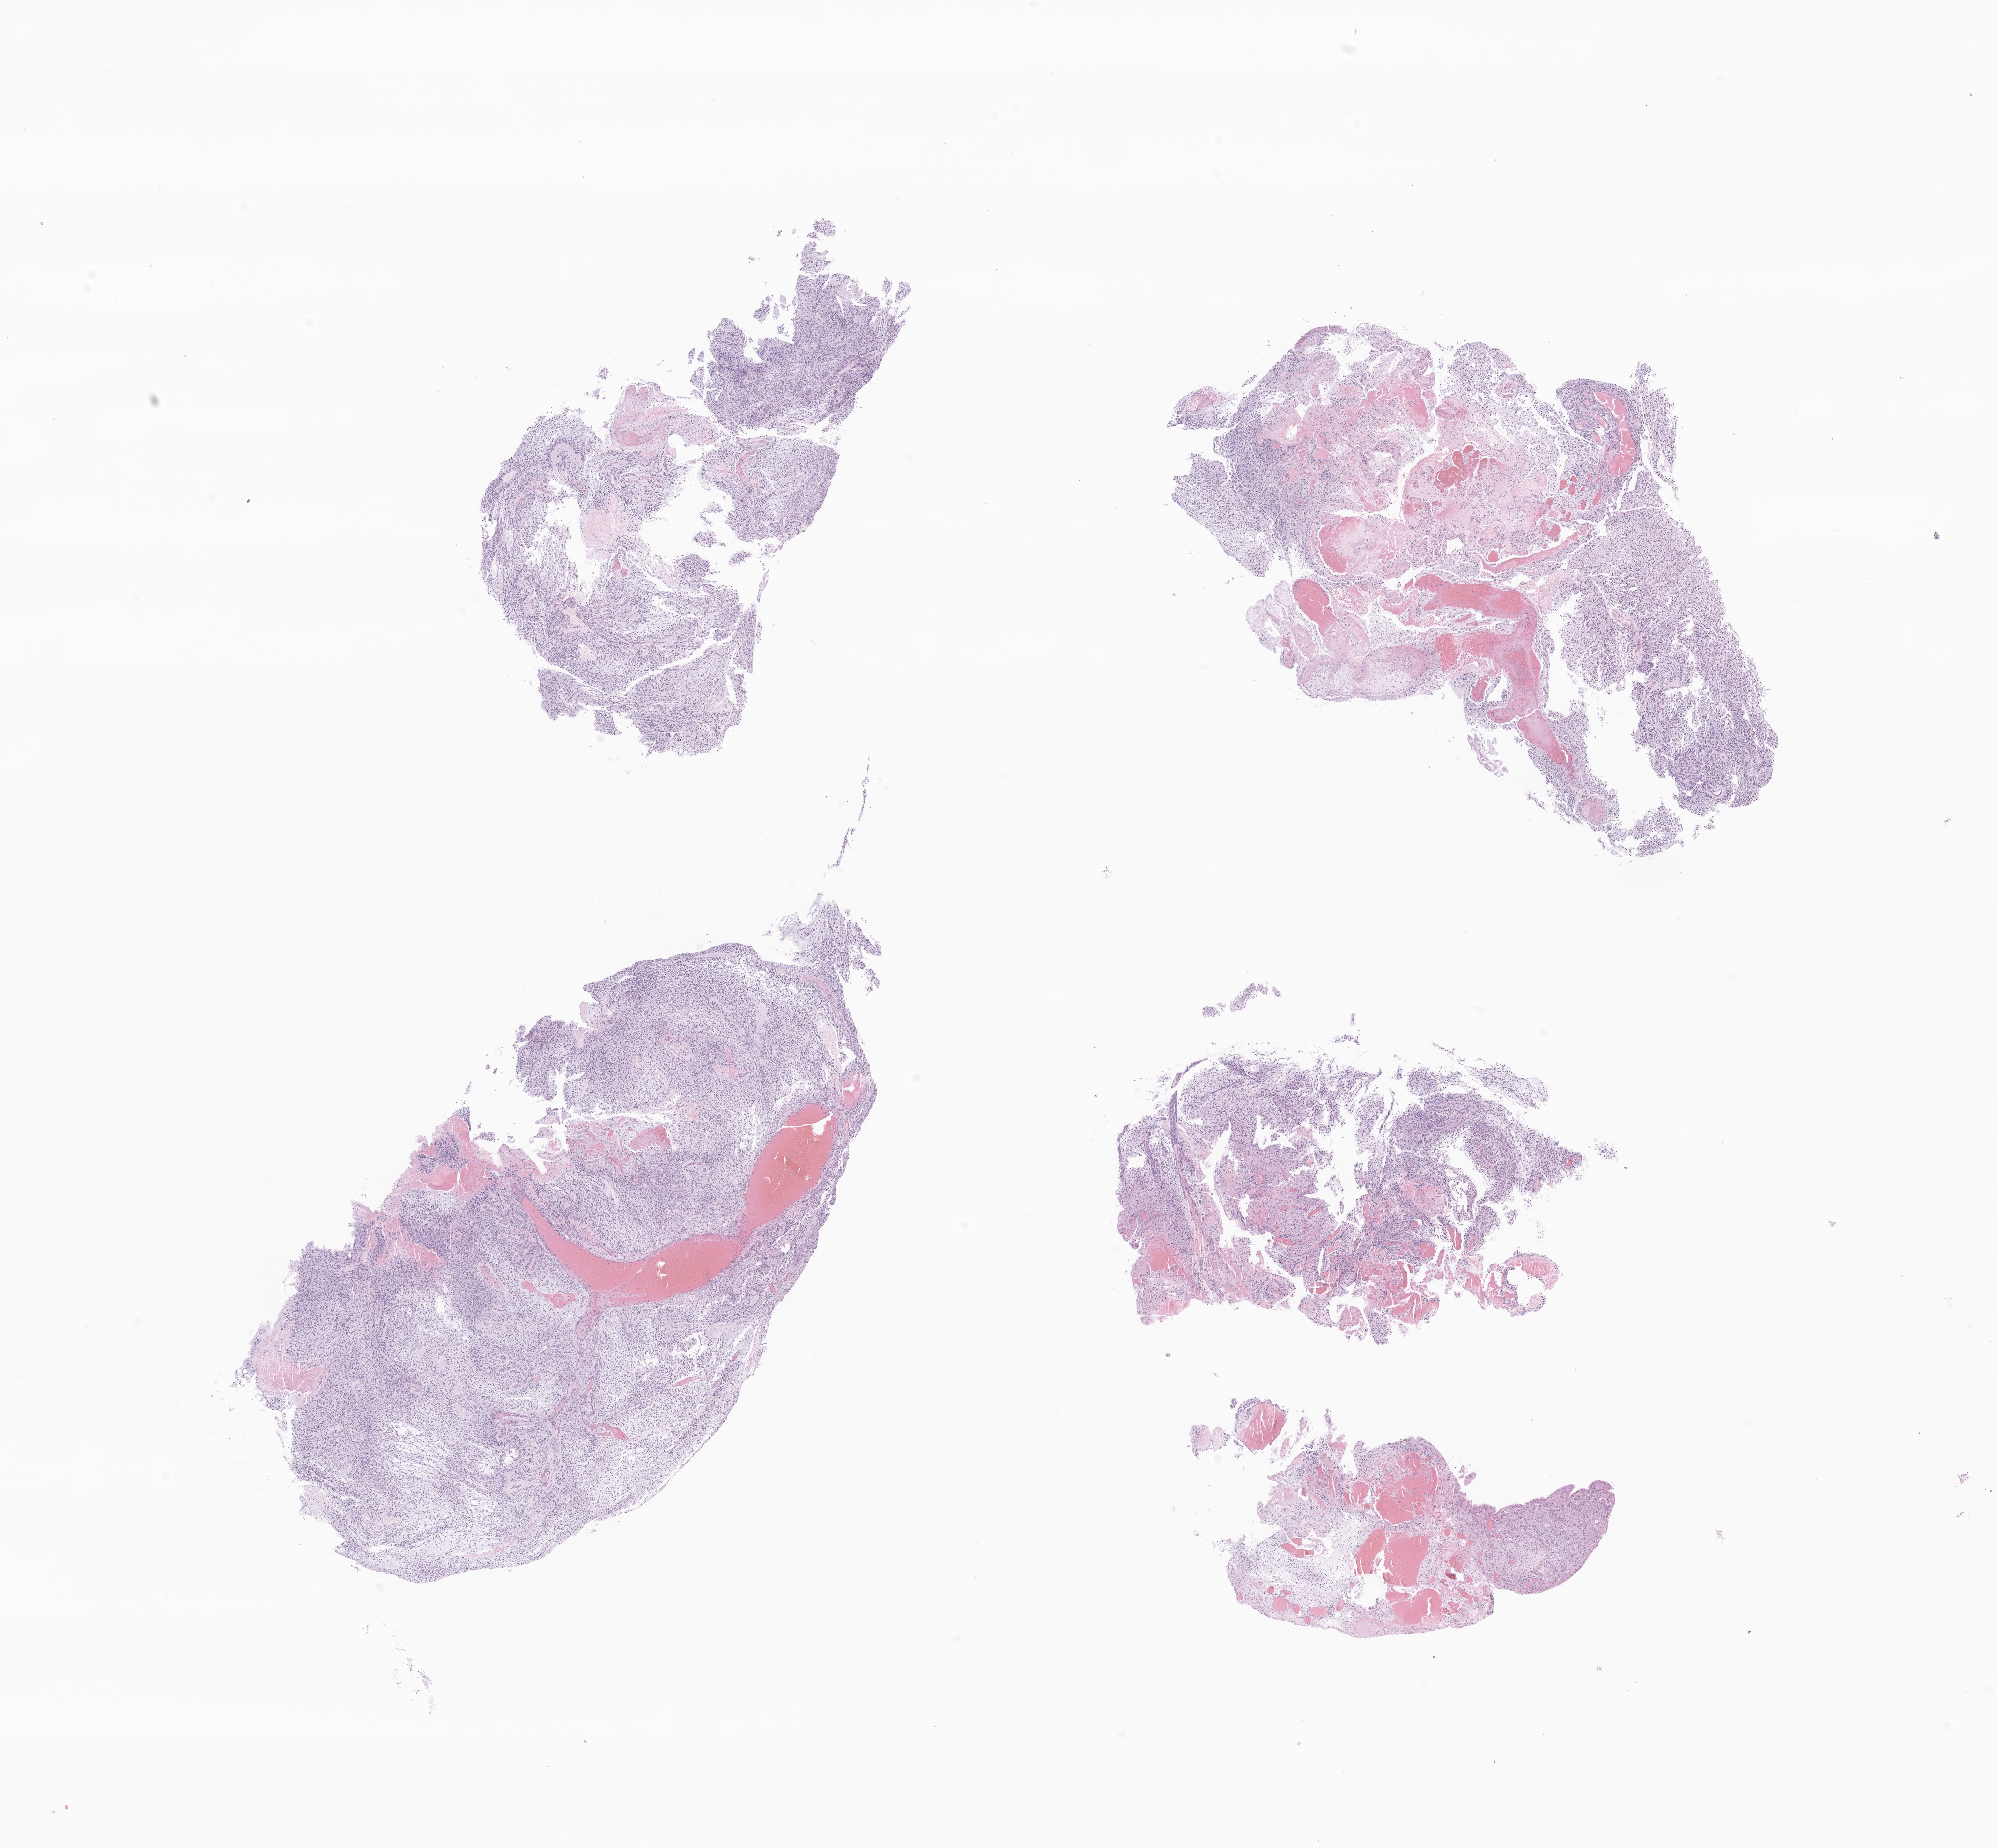
Haematoxylin and eosin whole-slide image of tumor tissue from the brain, a low-resolution overview of the entire scanned area, about 18.0 x 16.6 mm; formalin-fixed paraffin-embedded section. Patient female; age 297 days.
Diagnosis: Neoplasm, malignant.